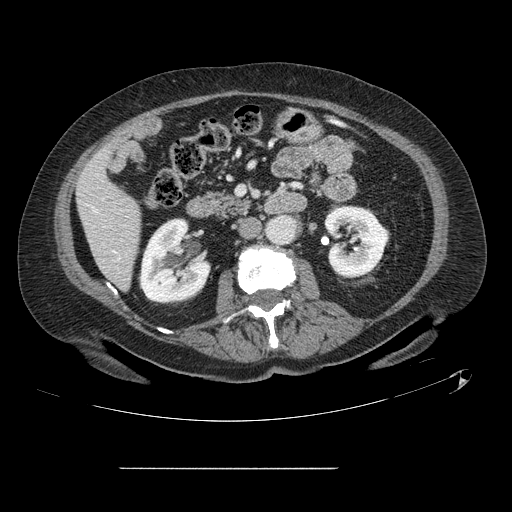
Contrast-enhanced abdominal CT, one axial slice. Slice 37 of 148 in the series (ordered by position). 120 kVp. Intravenous contrast given. Soft-tissue window (W 400 / L 40 HU). 2.5 mm slice thickness. 512 × 512 image matrix, field of view 439 × 439 mm. Female patient, age 75 years. From the clinical record (not read from this slice): diagnosis: colorectal cancer liver metastases, imaged before liver resection; multiple liver metastases: no; largest metastasis: 2.4 cm; disease in both lobes: no.
Outlined on this slice (outlined manually by an expert reader):
- liver: box from (x=78, y=150) to (x=140, y=289) px
- planned liver remnant (the part of the liver to remain after resection): (x=78, y=150)–(x=140, y=289)